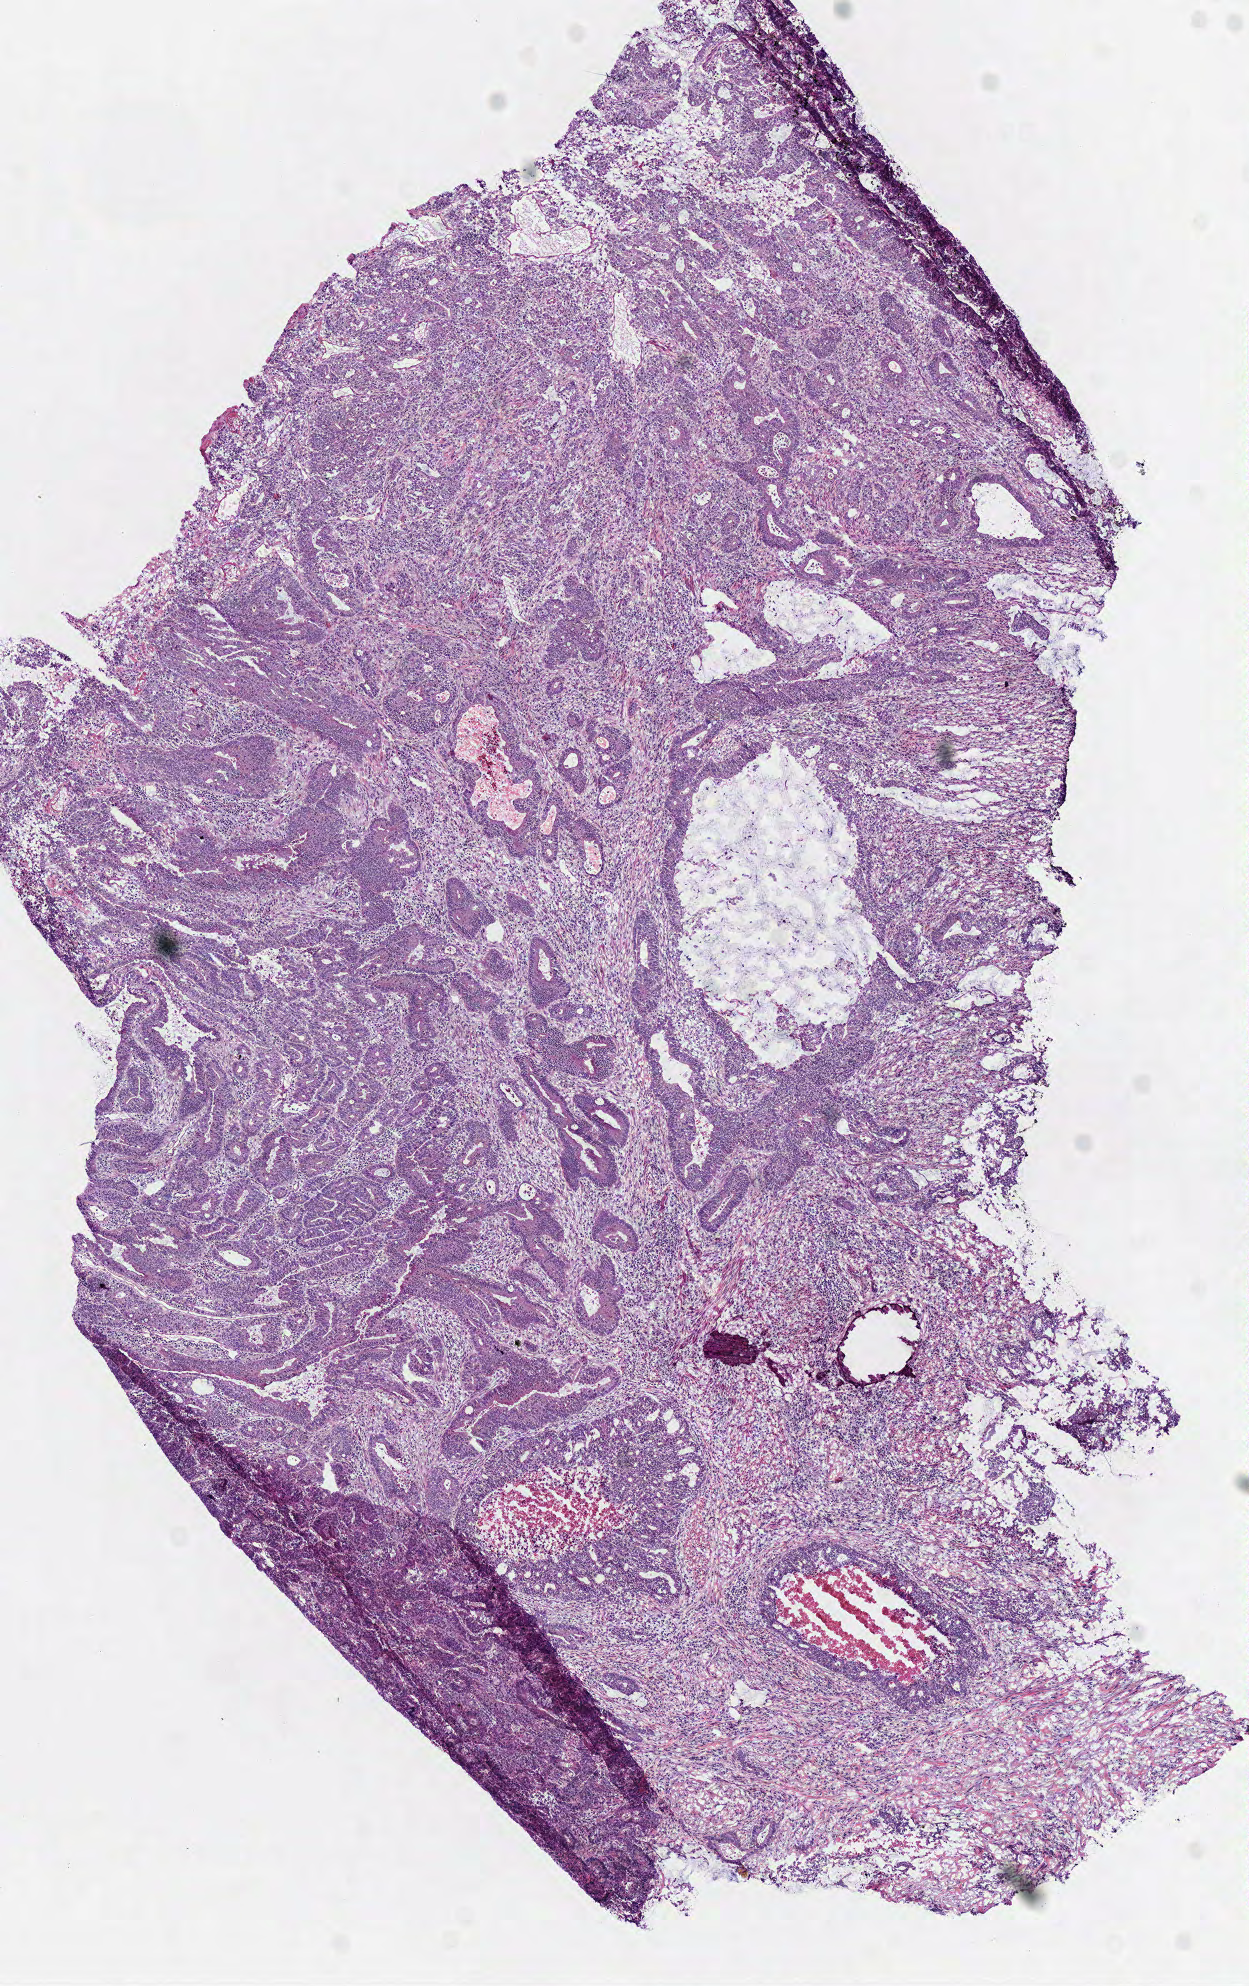
Digitized Hematoxylin and eosin (H&E) stained tissue section (whole slide), shown as a low-resolution overview of the whole scanned area (about 4.9 x 7.8 mm), frozen section from the top of the tissue portion, colon, primary tumour sample. Male patient; age at initial diagnosis 84 years.
Diagnosis: Mucinous adenocarcinoma.